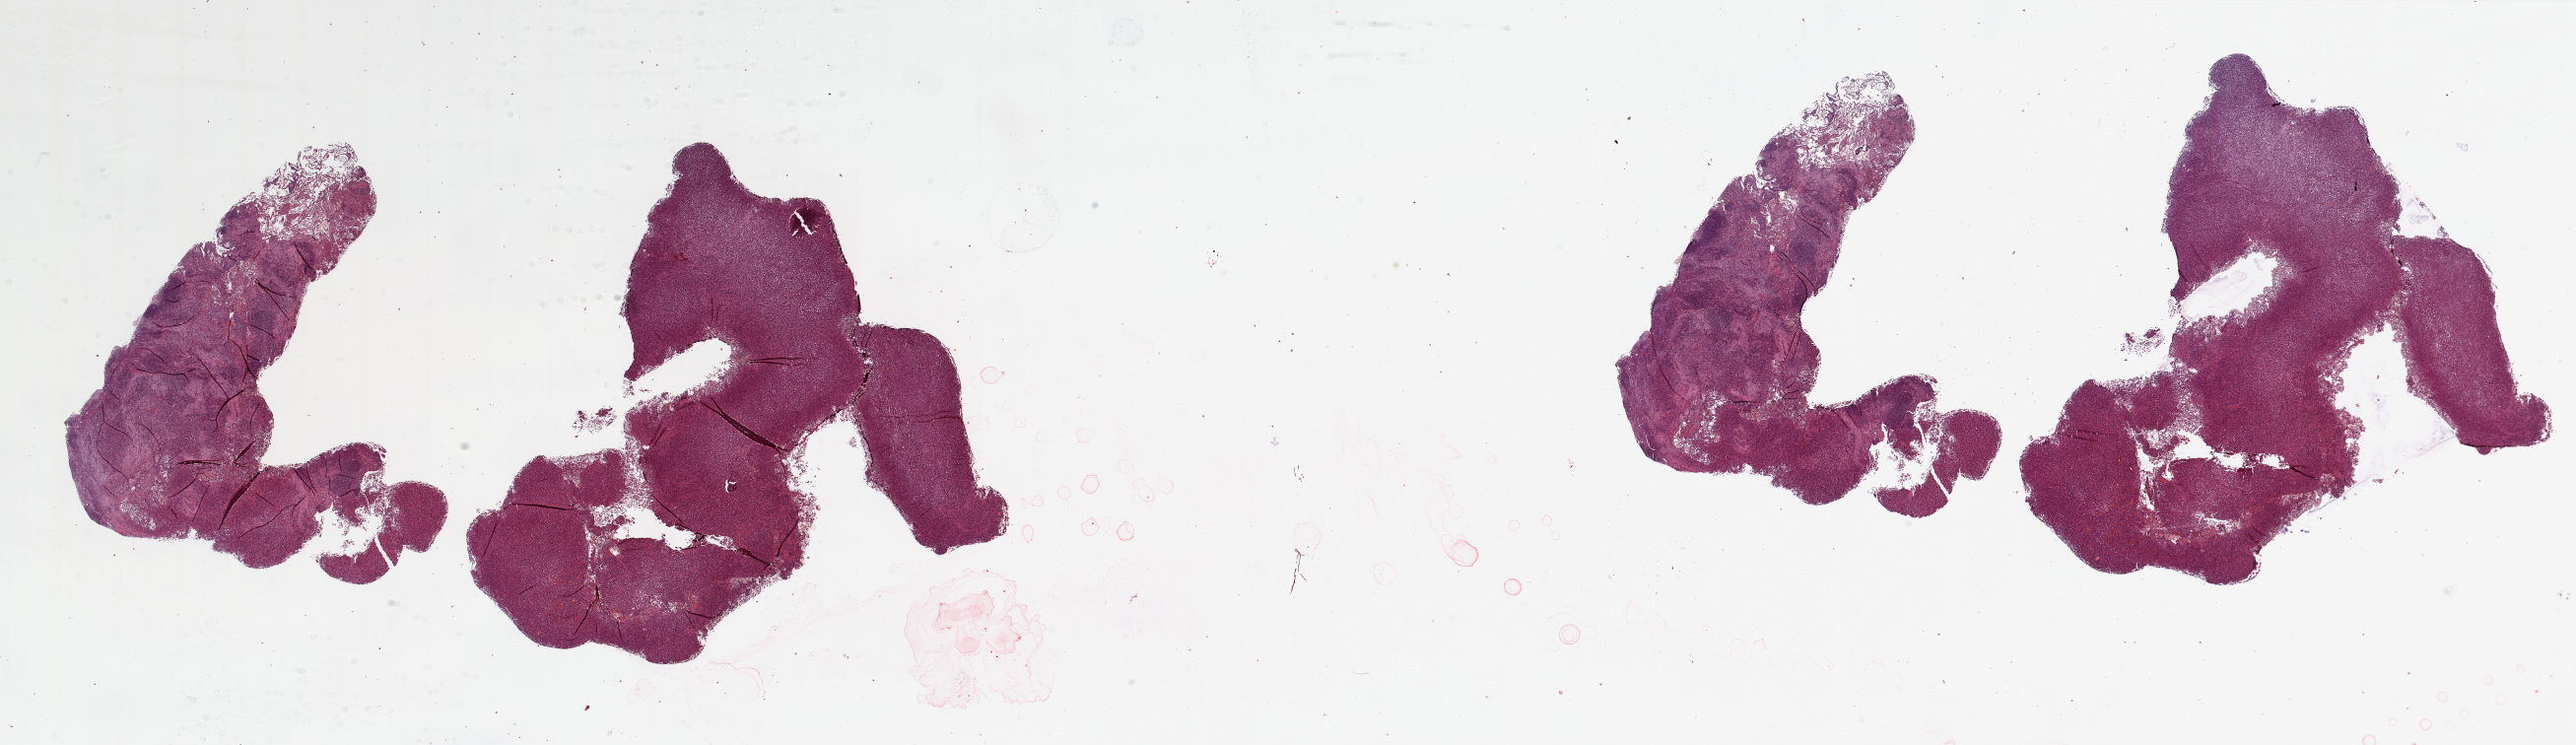
H&E whole-slide image — low-resolution overview of the scanned area, about 41.3 x 12.0 mm (from a 20x scan). Tumour tissue sample, sampled site: lung. Patient: male, age 56 years.
Histologic diagnosis: Adenocarcinoma, NOS.